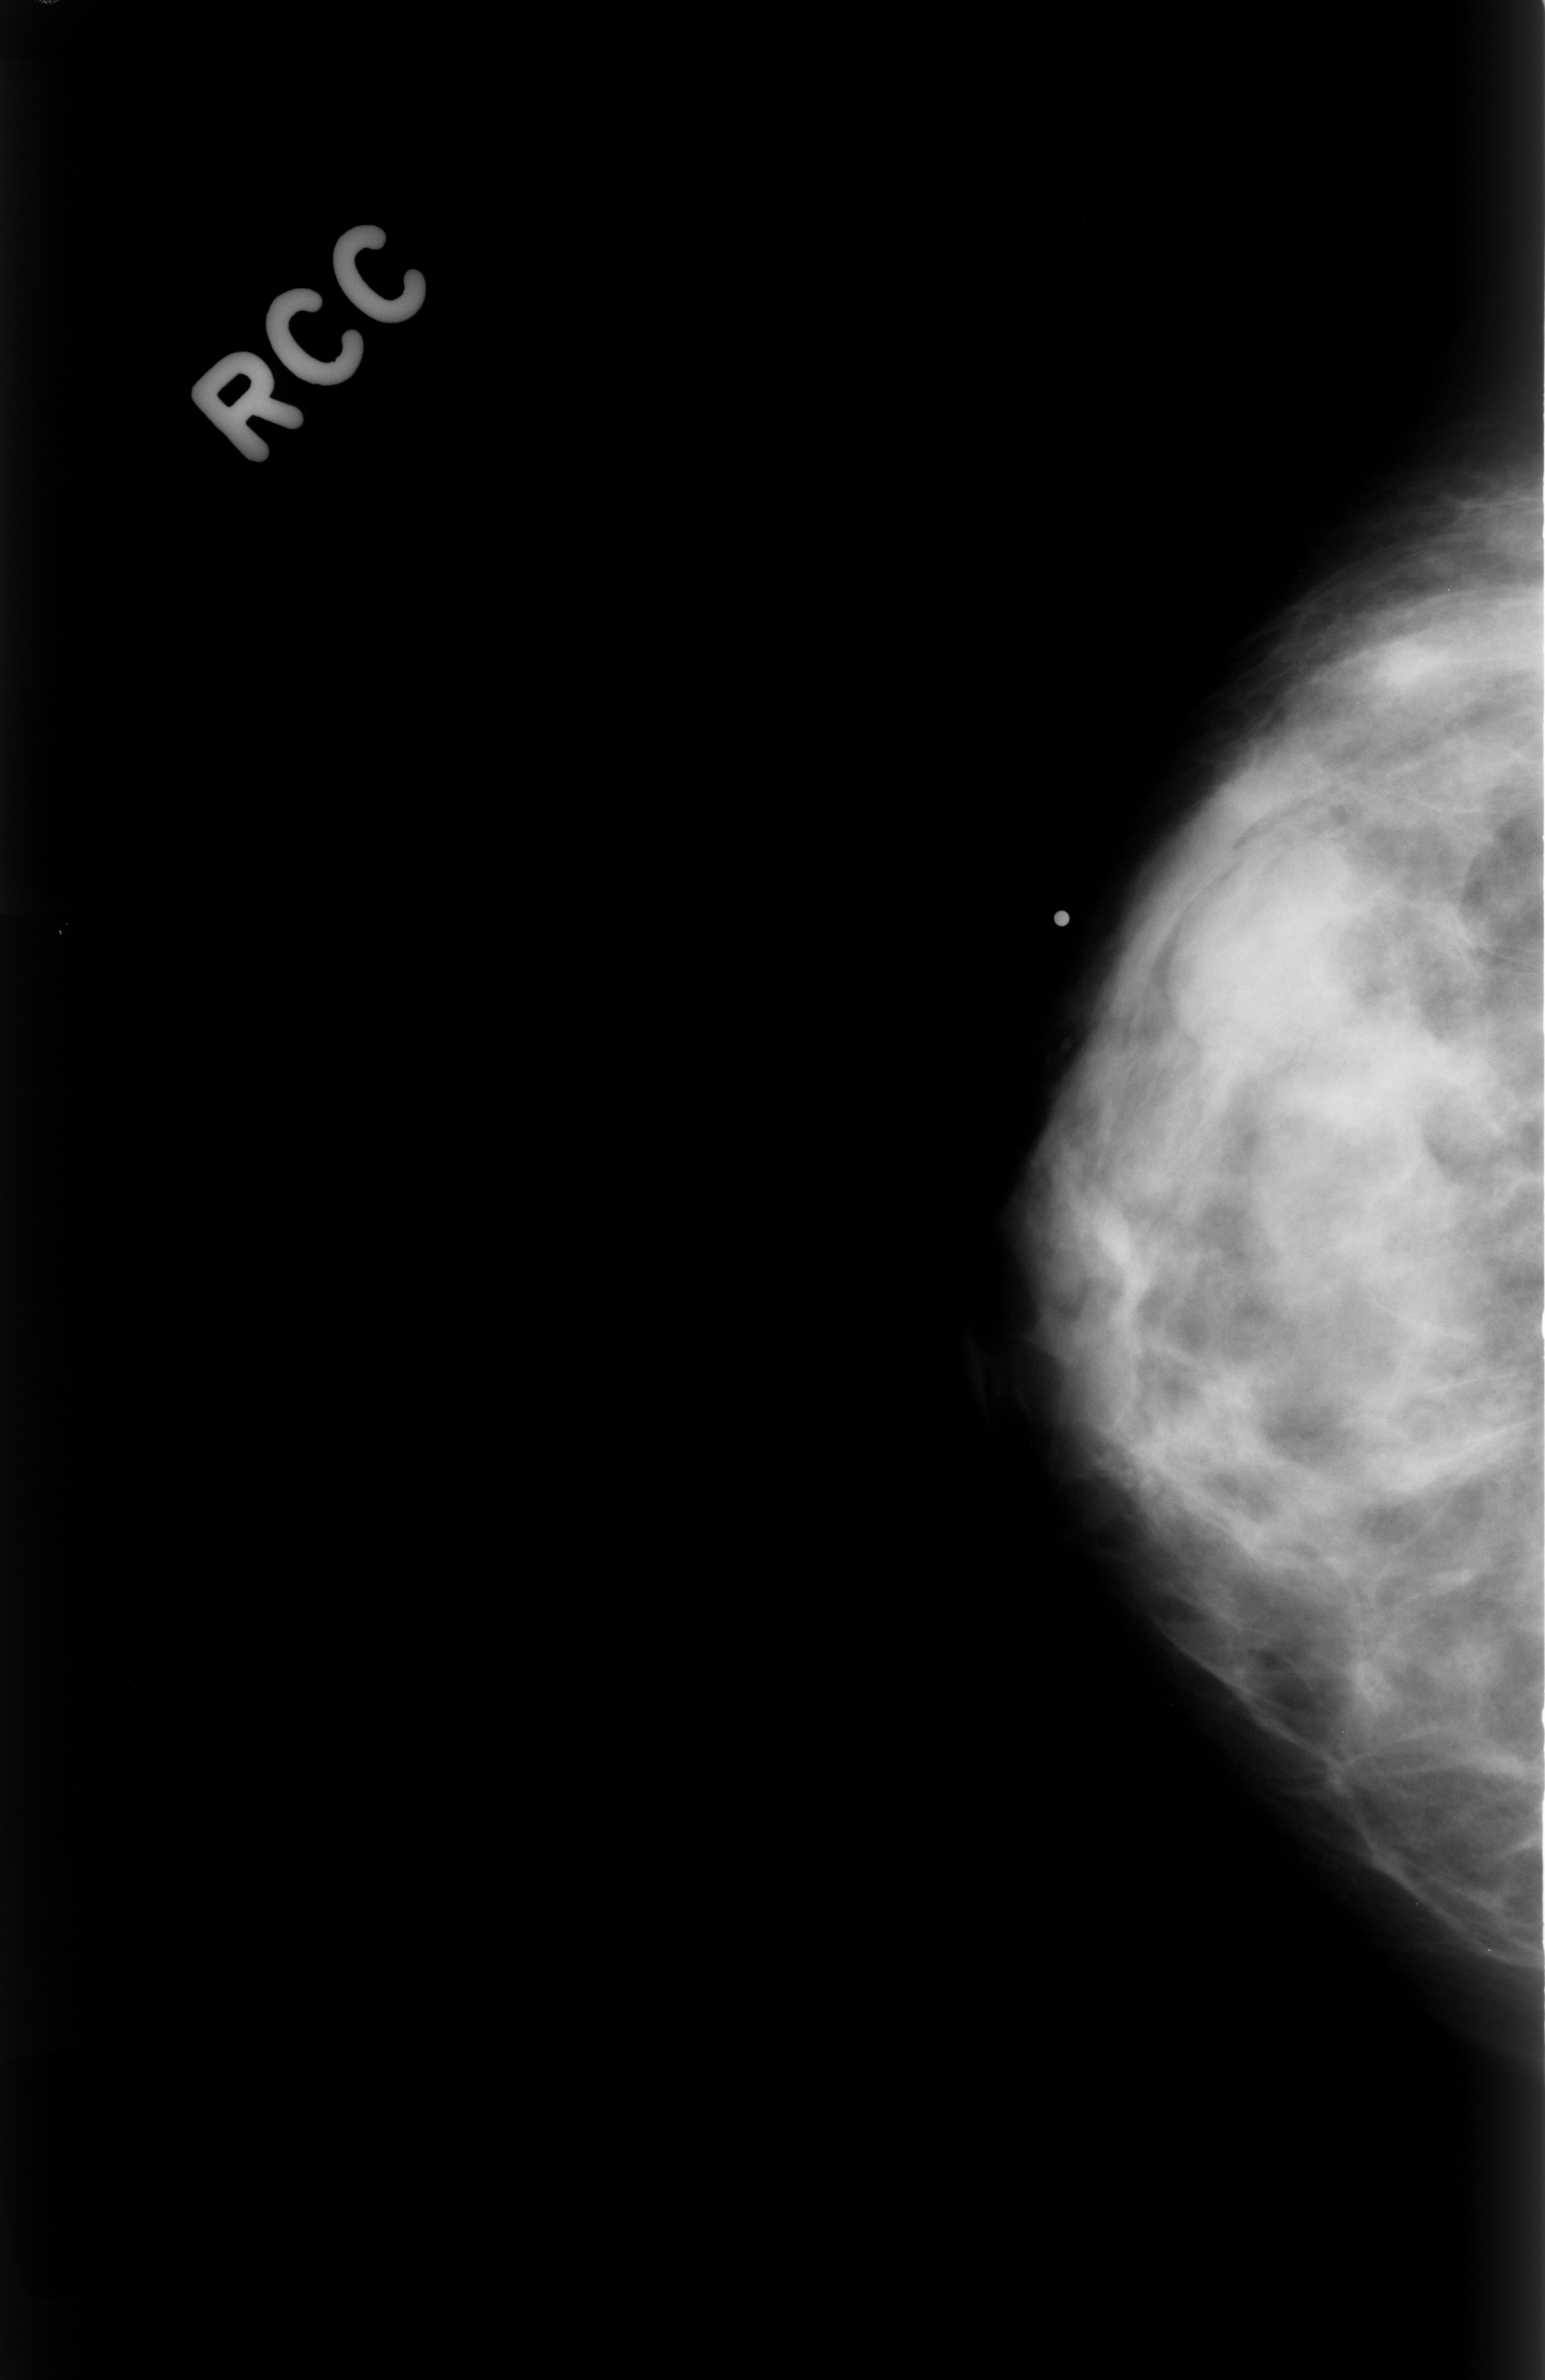
Mammogram (digitized film). Right breast. Craniocaudal (CC) view. BI-RADS breast density category 3 (scale 1–4). 1545 × 2380 image matrix.
Marked abnormalities (boxes around the expert regions of interest):
- mass, shape oval, margins obscured; BI-RADS assessment category 3; subtlety rating 4 on a 1 (subtle) to 5 (obvious) scale; pathology result (as recorded, not read from the image): benign: bounding box (x1, y1, x2, y2) in pixels: (1174, 847, 1379, 1051)